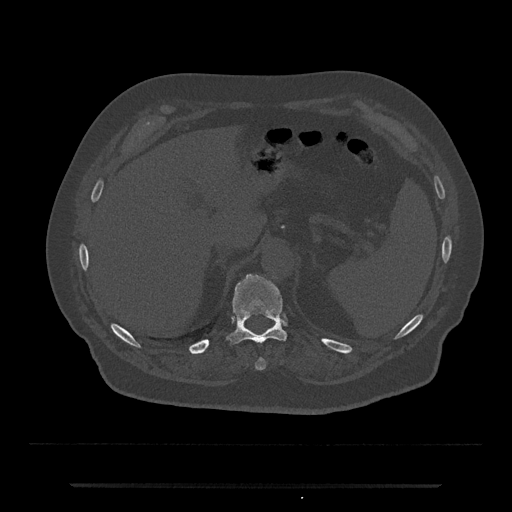
CT including the spine, one axial slice. Position 653 of 797 along the scan axis. Reconstruction kernel Br40s/3. Bone window (W 1800 / L 400 HU). 512 × 512 image matrix, field of view 434 × 434 mm. Male patient, age 80 years. From the clinical record (not read from this slice): primary cancer: prostate.
Structures marked on this image (semi-automatically segmented with operator editing):
- T10 vertebra: bounding box [x1, y1, x2, y2] px = [256, 358, 266, 370]
- T11 vertebra: [228, 274, 286, 344]